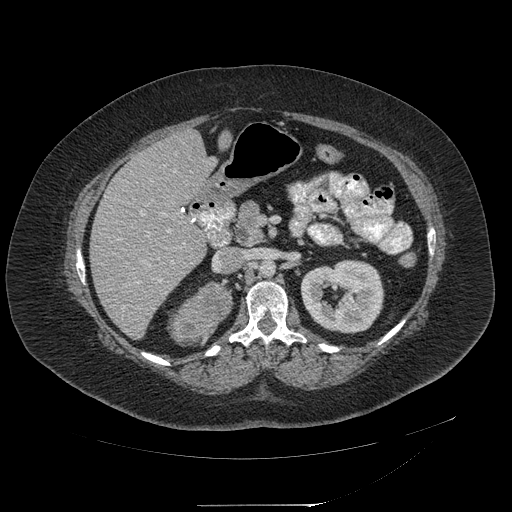
Contrast-enhanced abdominal CT, one axial slice; position 113 of 217 along the scan axis; reconstruction kernel STANDARD; intravenous contrast given; soft-tissue window (W 400 / L 40 HU); 512 × 512 image matrix, field of view 453 × 453 mm. Patient: female, 55 years. Case-level facts recorded for this patient, not image findings: diagnosis: adrenocortical carcinoma; tumour side: right adrenal; tumour size at pathology: 11 cm; Ki-67 index: 20 %; stage (as recorded): 2.
Outlined on this slice (semi-automatically segmented with operator editing):
- mass: box from (x=170, y=284) to (x=231, y=345) px